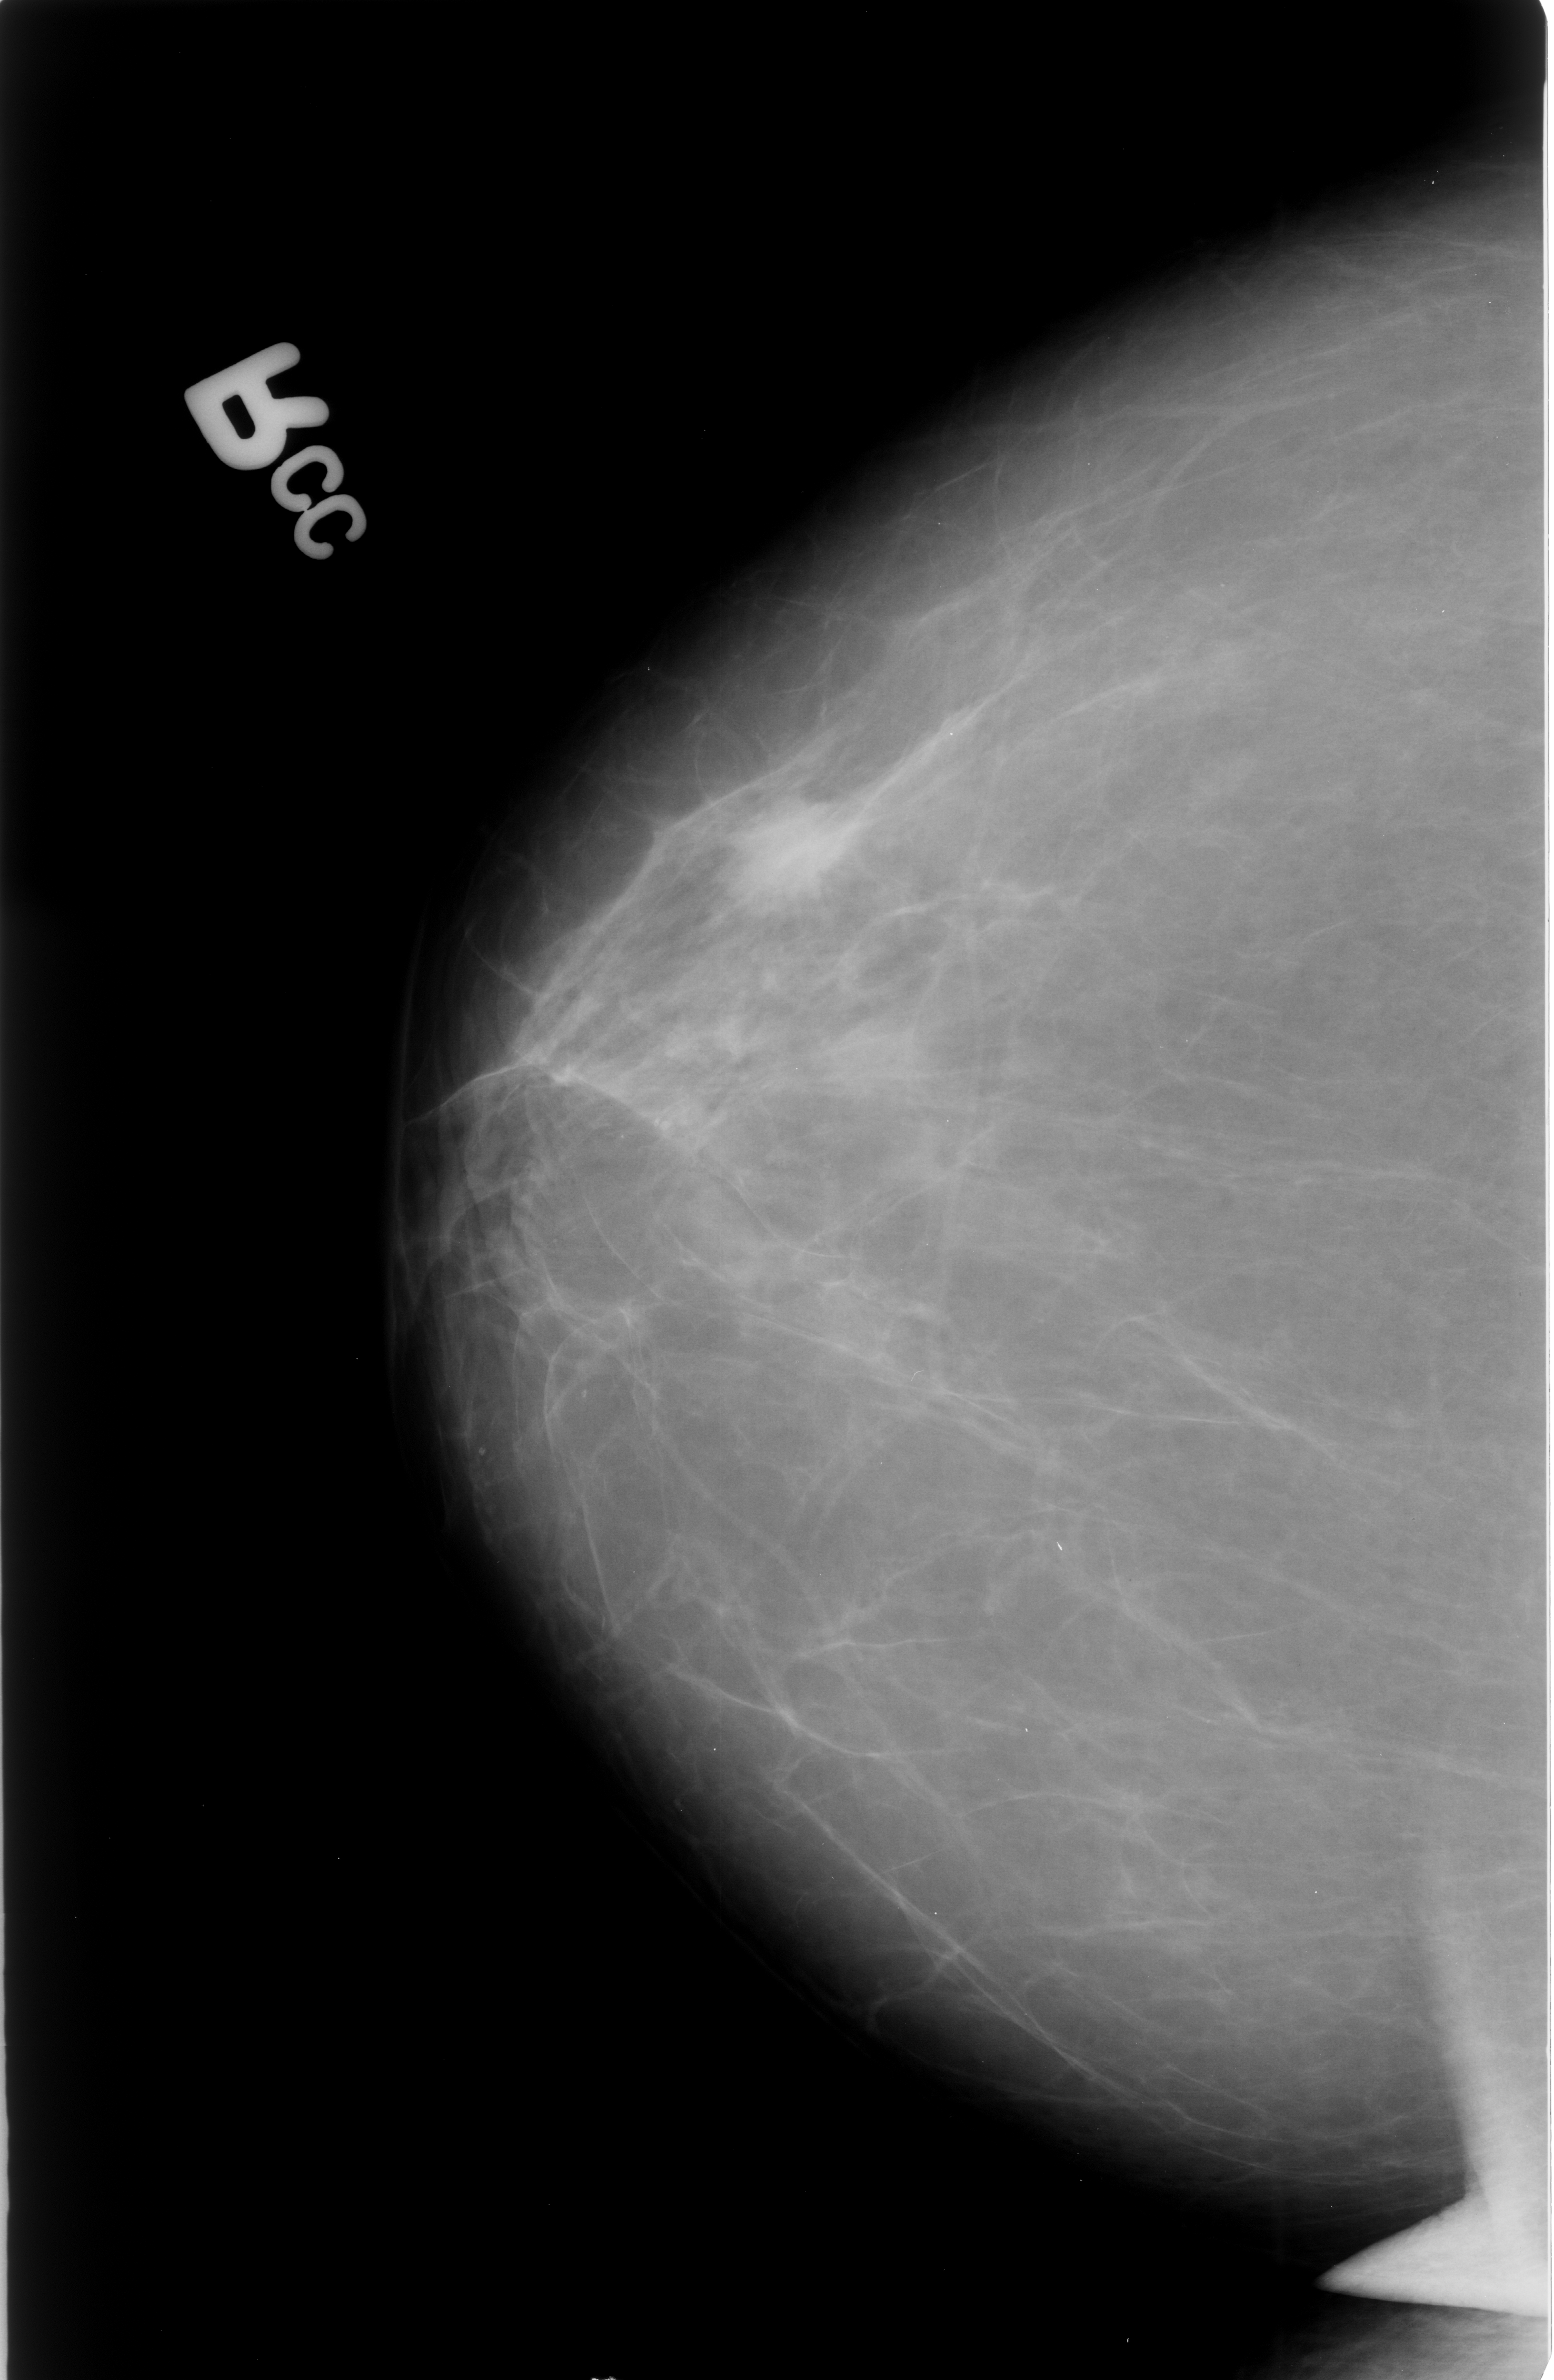
Scanned film-screen mammogram. Right breast. CC view. 1554 × 2380 image matrix.
Expert-marked regions of interest on this image (one box per marked abnormality):
- mass, shape irregular, margins ill defined / spiculated; BI-RADS assessment category 4; subtlety rating 3 on a 1 (subtle) to 5 (obvious) scale; pathology (as recorded): malignant: box from (x=709, y=795) to (x=846, y=921) px